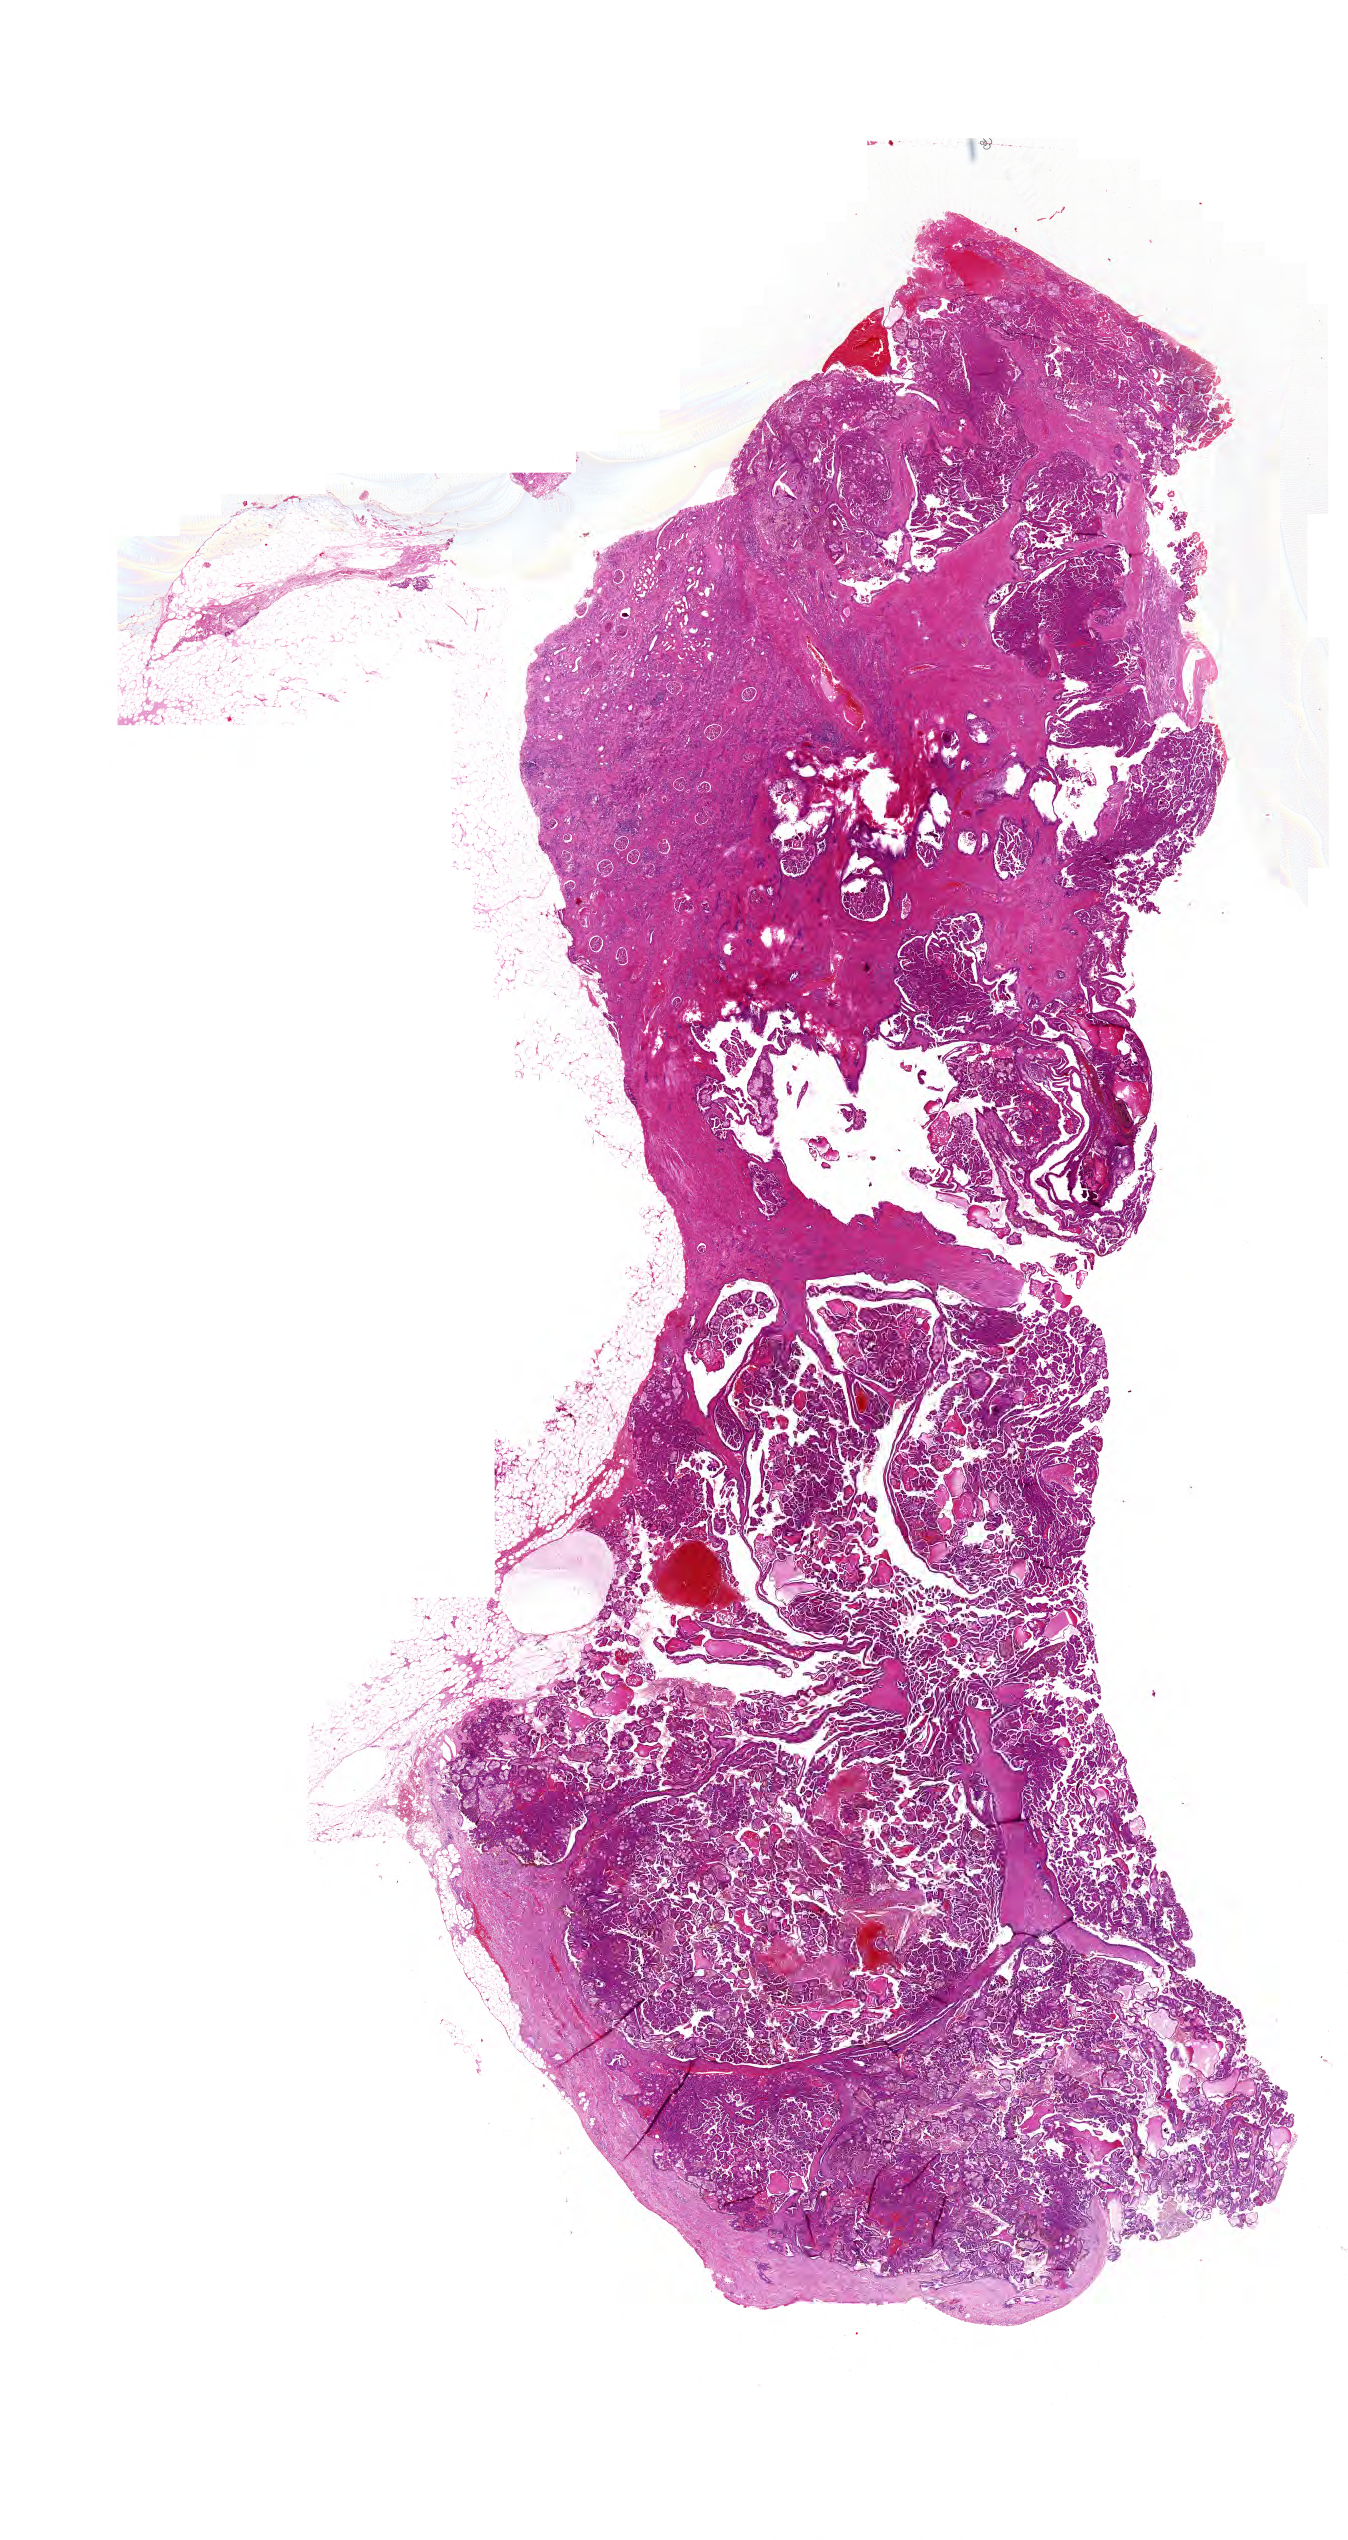
Hematoxylin and eosin (H&E) stained whole-slide image — whole scanned area (about 16.8 x 31.6 mm) shown as a low-resolution overview. FFPE section. Kidney, primary tumour sample. Patient: male, age at initial diagnosis 75 years.
Laterality: right. Pathologic diagnosis: Papillary adenocarcinoma, NOS.